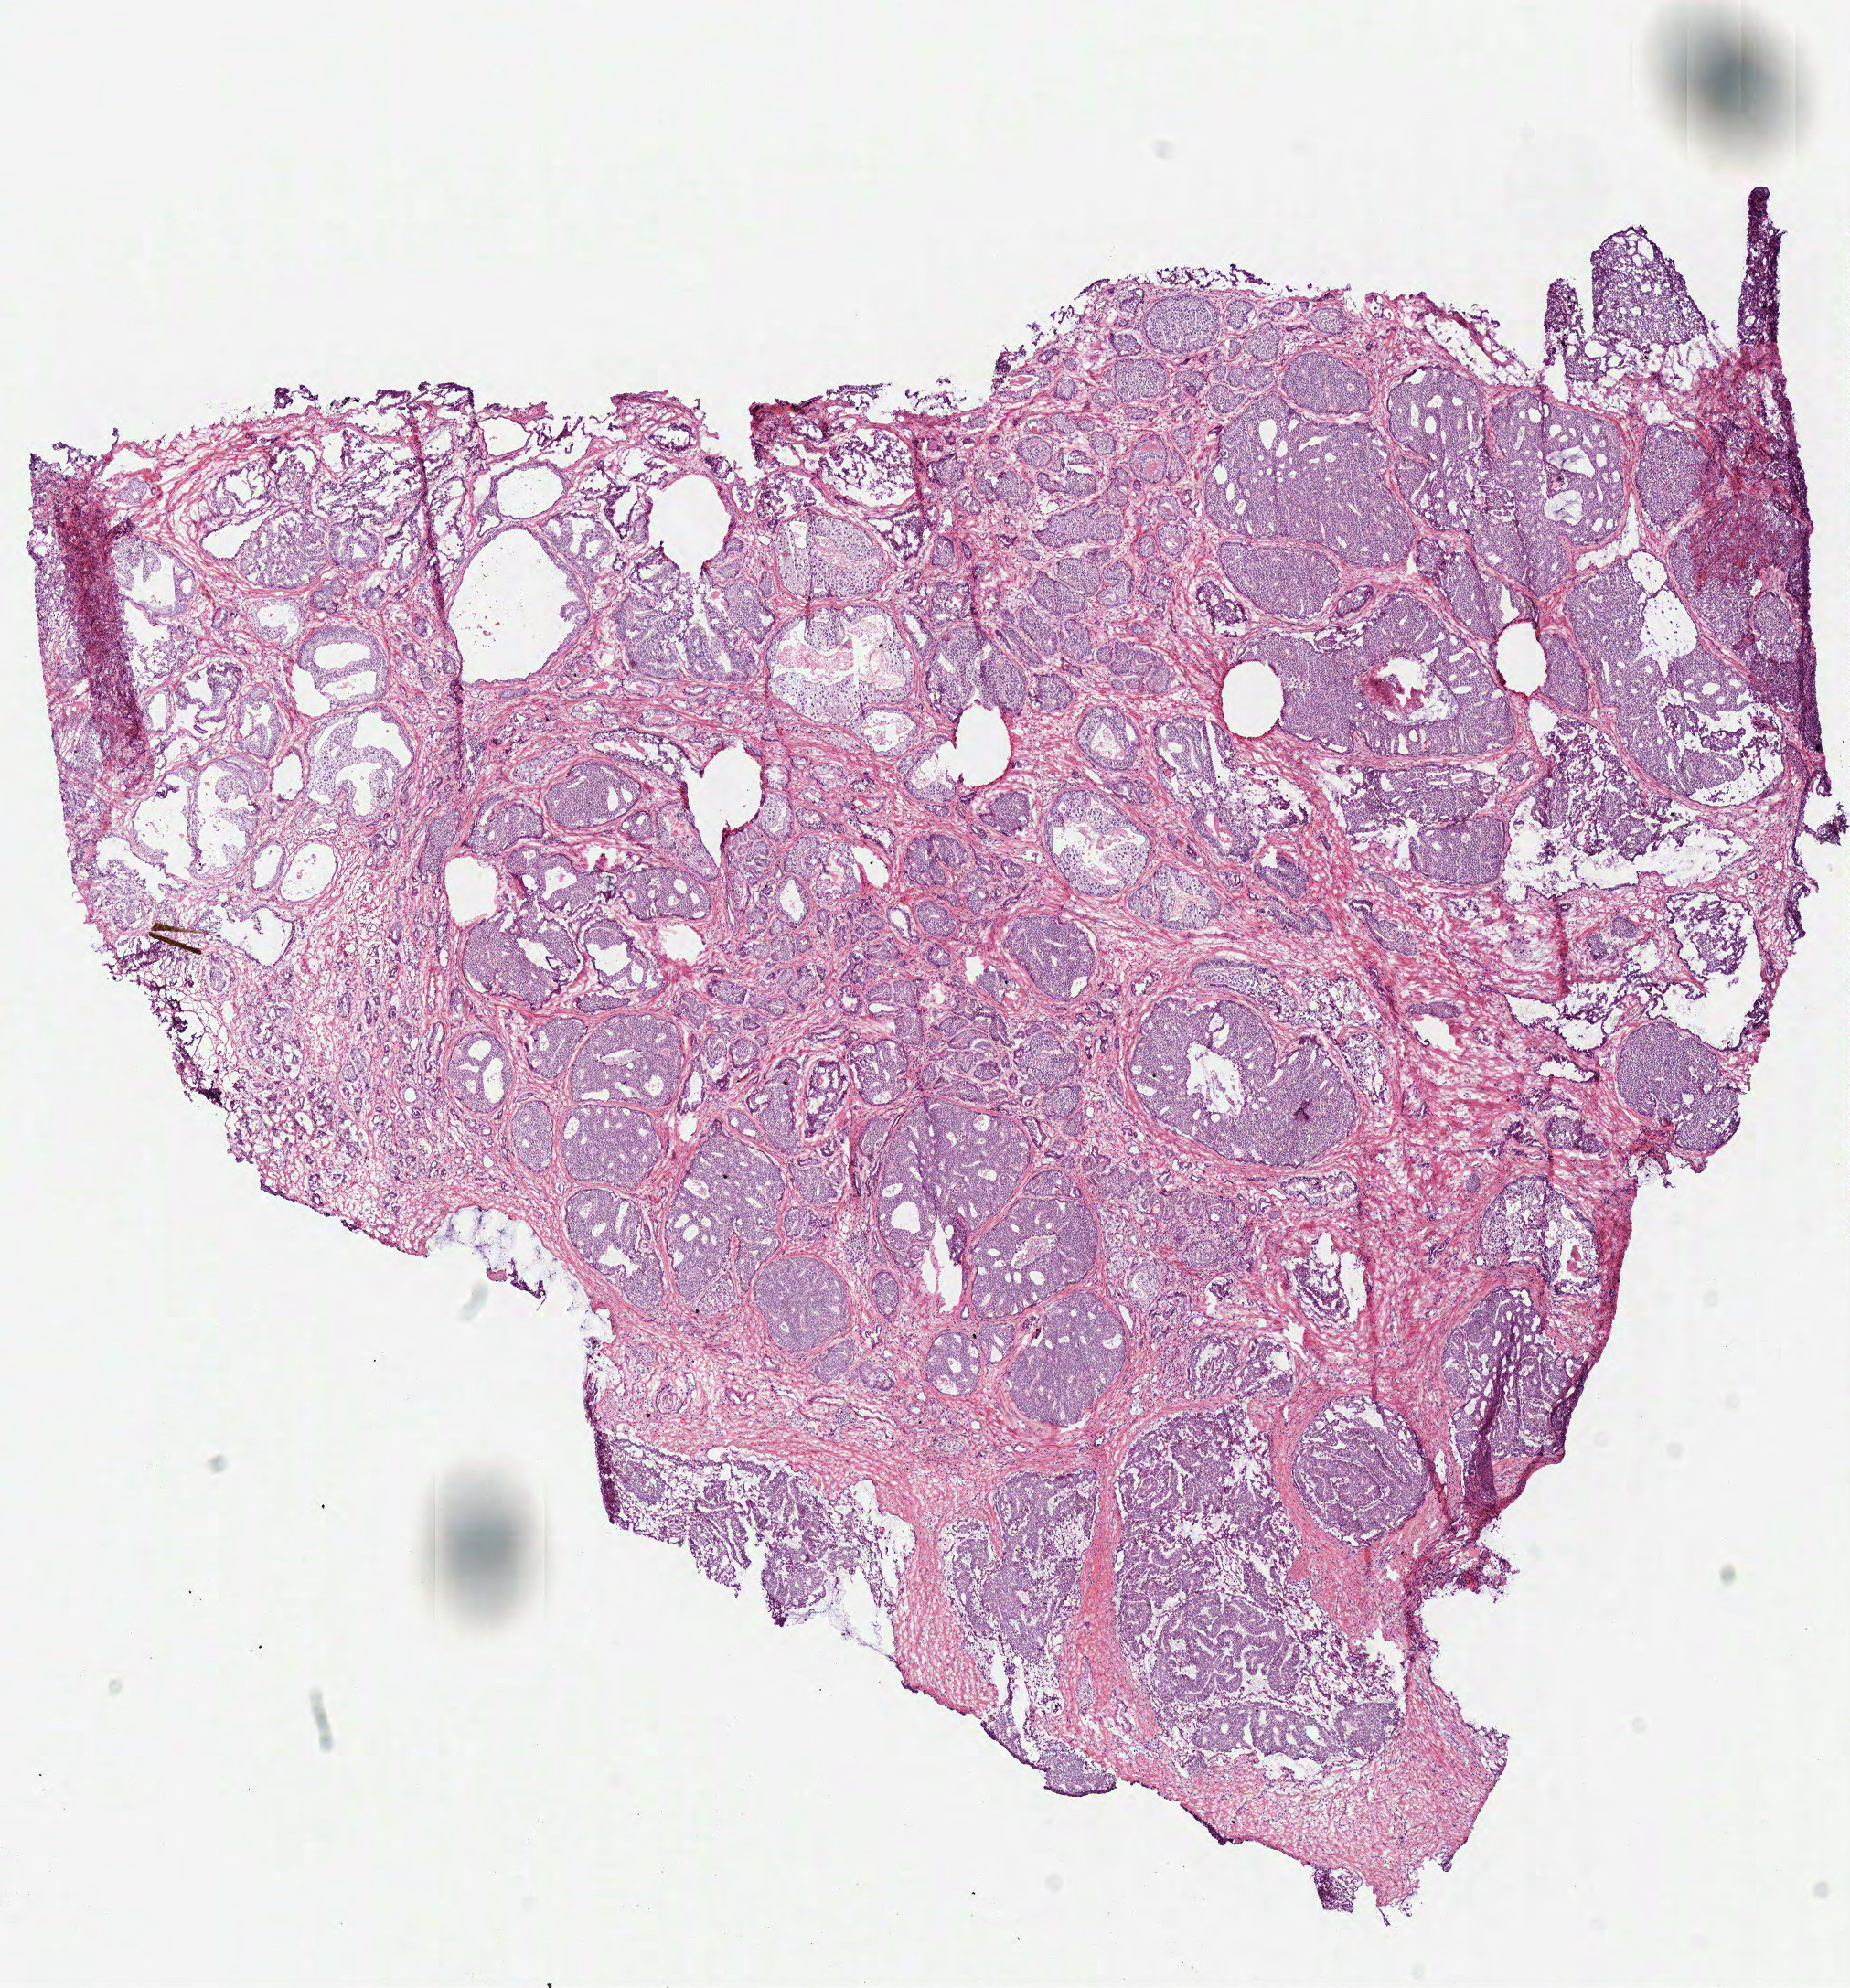
Whole-slide histology image, Hematoxylin and eosin (H&E) stained, shown as a low-resolution overview of the whole scanned area (about 8.0 x 8.6 mm, from a 40x scan), frozen section from the top of the tissue portion, prostate, primary tumour sample. Patient: male, age at initial diagnosis 56 years. Gleason score: 7 (3+4). Composition of this section per pathologist review: tumour cells 75%, tumour nuclei 75%, normal cells 5%, stromal cells 18%, necrosis 2%.
- lymph nodes positive (case pathology): 0 of 4 examined
- histologic diagnosis: Acinar cell carcinoma (prostate gland)
- laterality: right